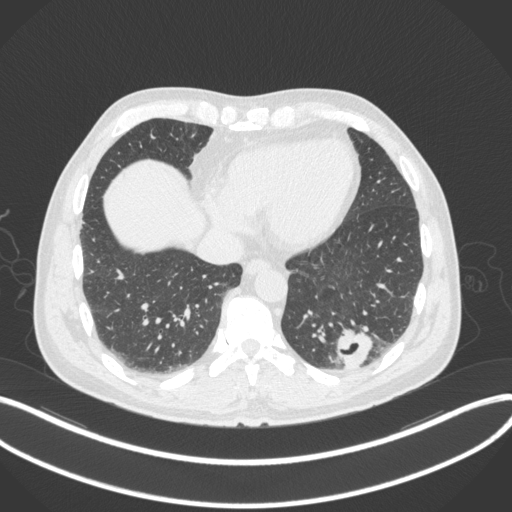
Chest CT, one axial slice; slice 78 of 313 in the series (ordered by position); reconstruction kernel B31f; 120 kVp; lung window (W 1500 / L -600 HU); 1 mm slice thickness; 512 × 512 image matrix, field of view 400 × 400 mm. Patient: male, 54 years. Case-level facts recorded for this patient, not image findings: clinical TNM (as recorded): T1c N0 M1; histopathological grade: G3.
Annotated regions visible in this slice (bounding box drawn by a radiologist):
- lung tumour (recorded histology: adenocarcinoma): bounding box [x1, y1, x2, y2] px = [334, 325, 376, 371]